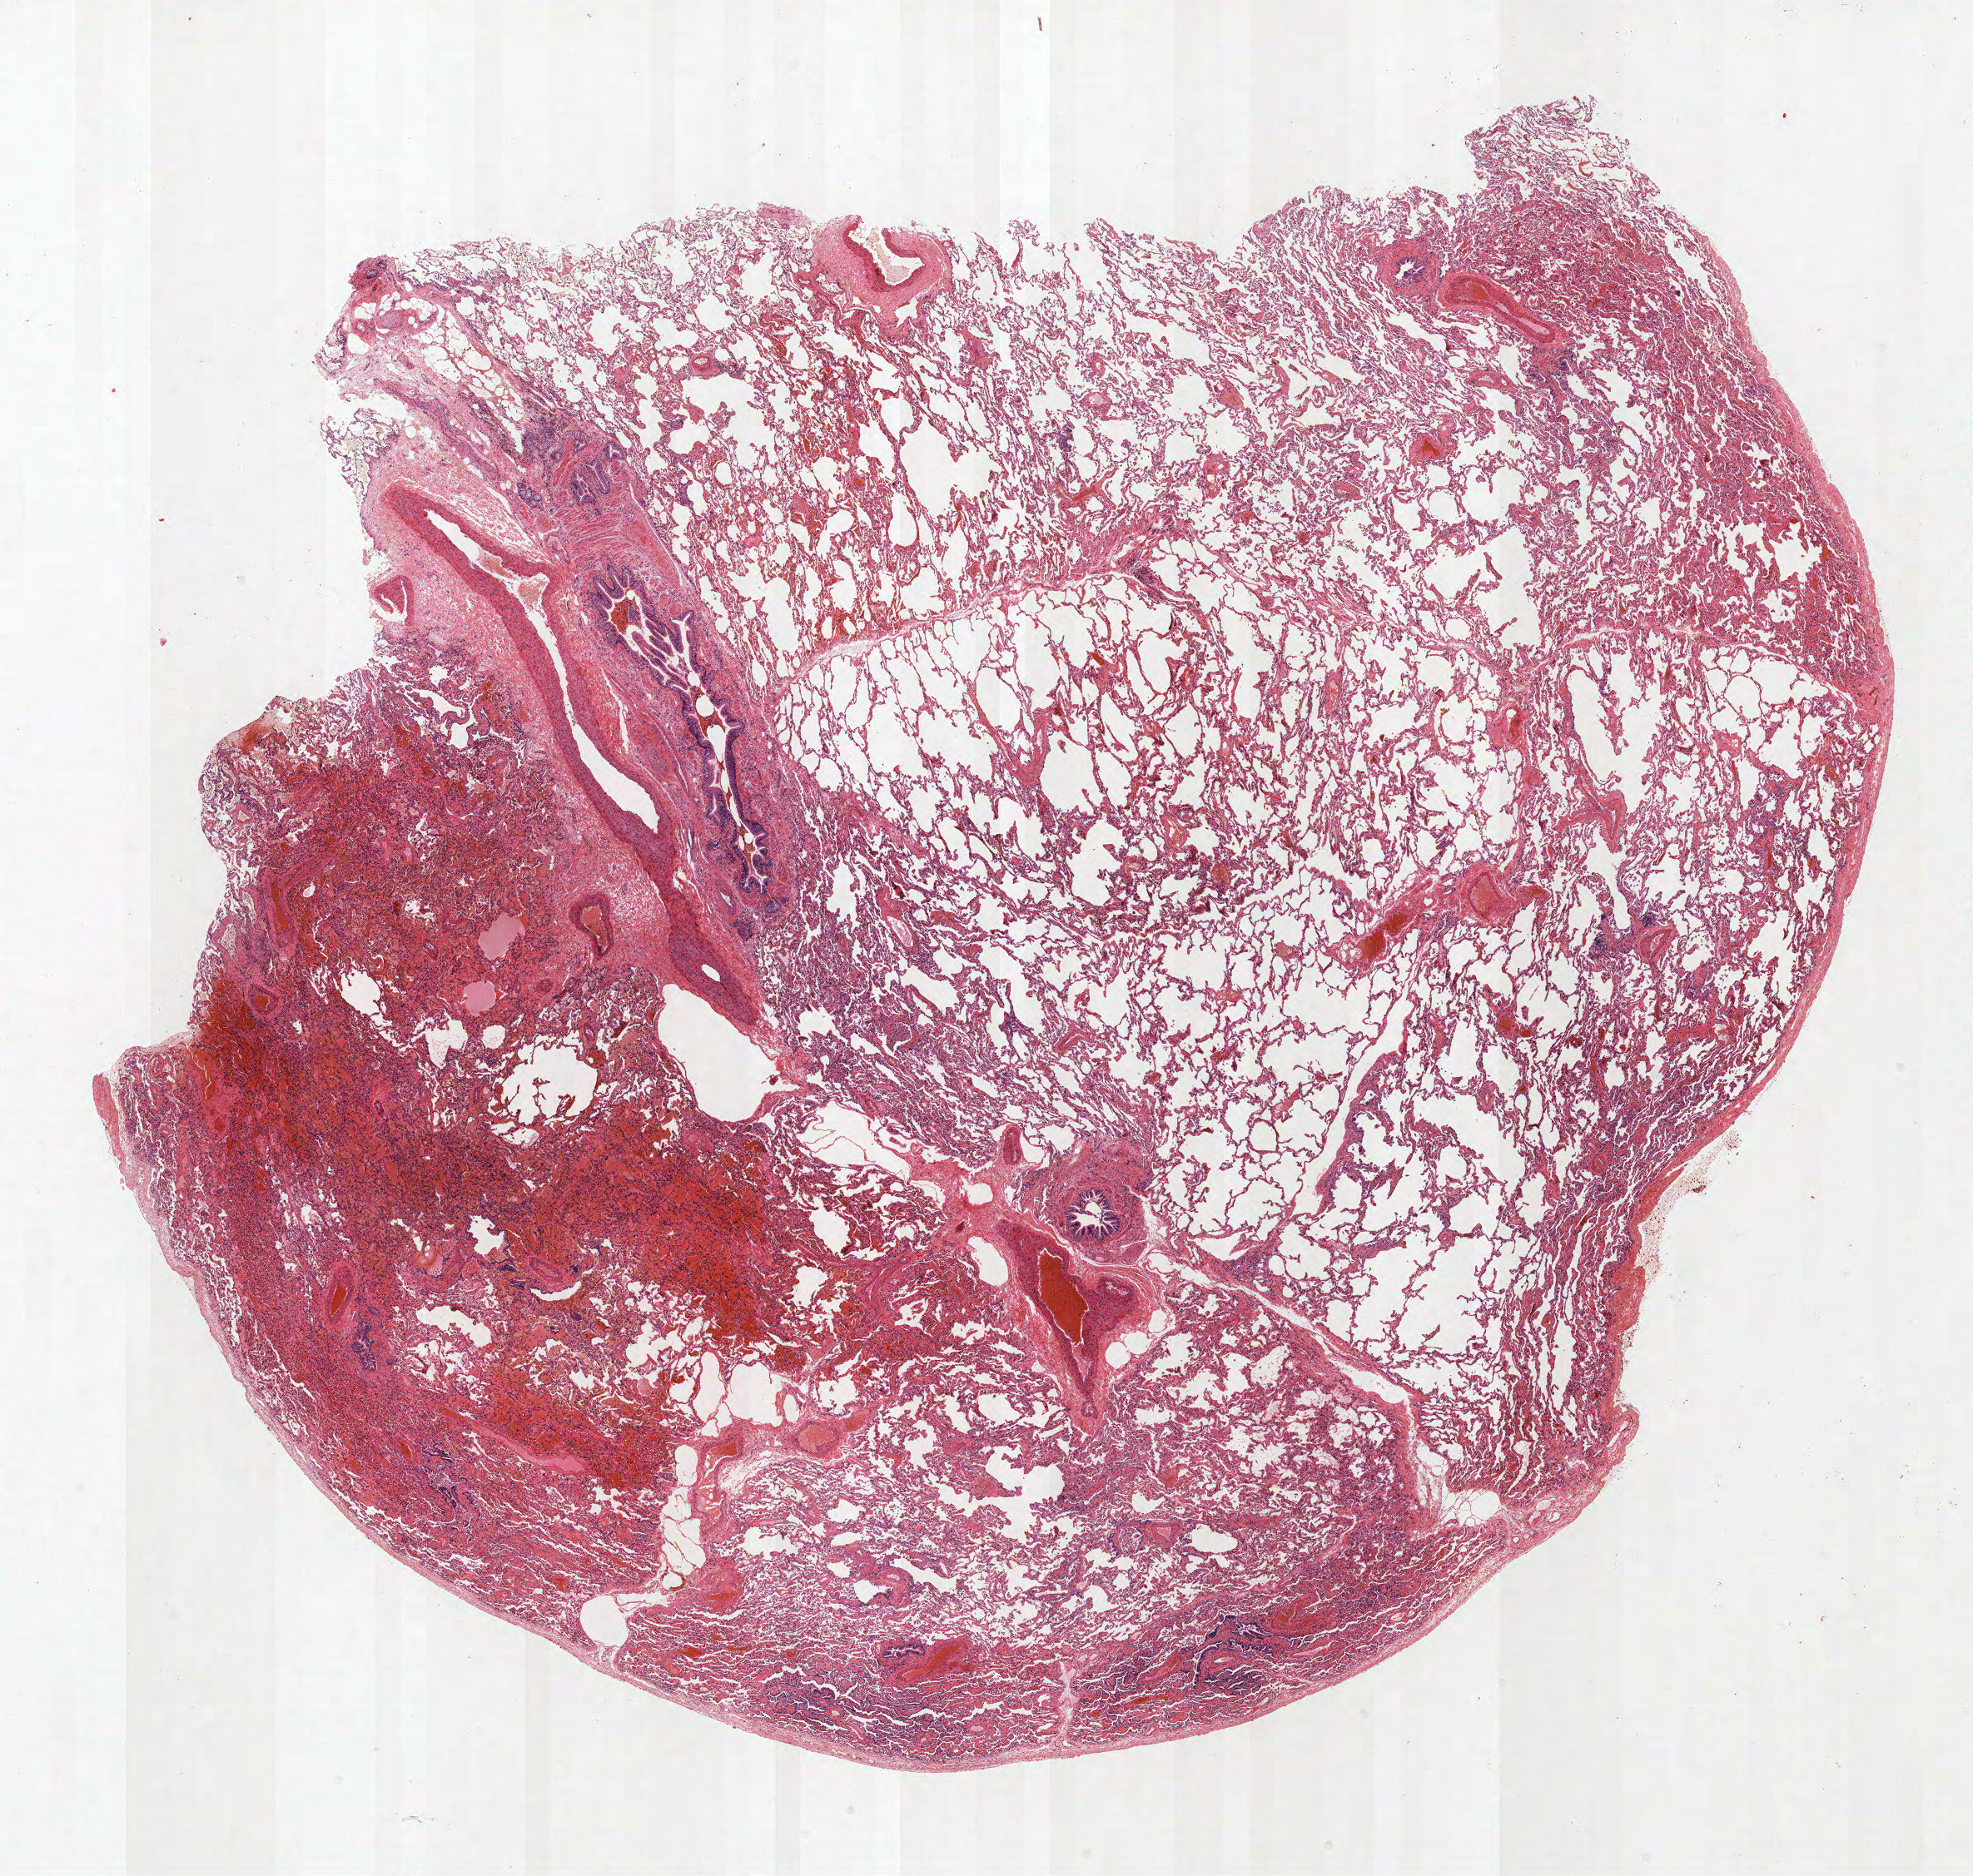
Whole-slide histology image, H&E-stained, low-resolution overview of the scanned area, about 19.0 x 18.0 mm (from a 40x scan), FFPE section, lung. Male patient, aged 55 at enrolment. Current smoker at enrolment. Grade: moderately differentiated (G2).
ICD-O-3 topography: upper lobe of lung (C34.1). Tumour size (pathology): 13 mm. Participant's lung-cancer diagnosis: Mucinous adenocarcinoma. Primary tumour location (clinical record): right upper lobe. Stage (AJCC 6th edition): IIB.